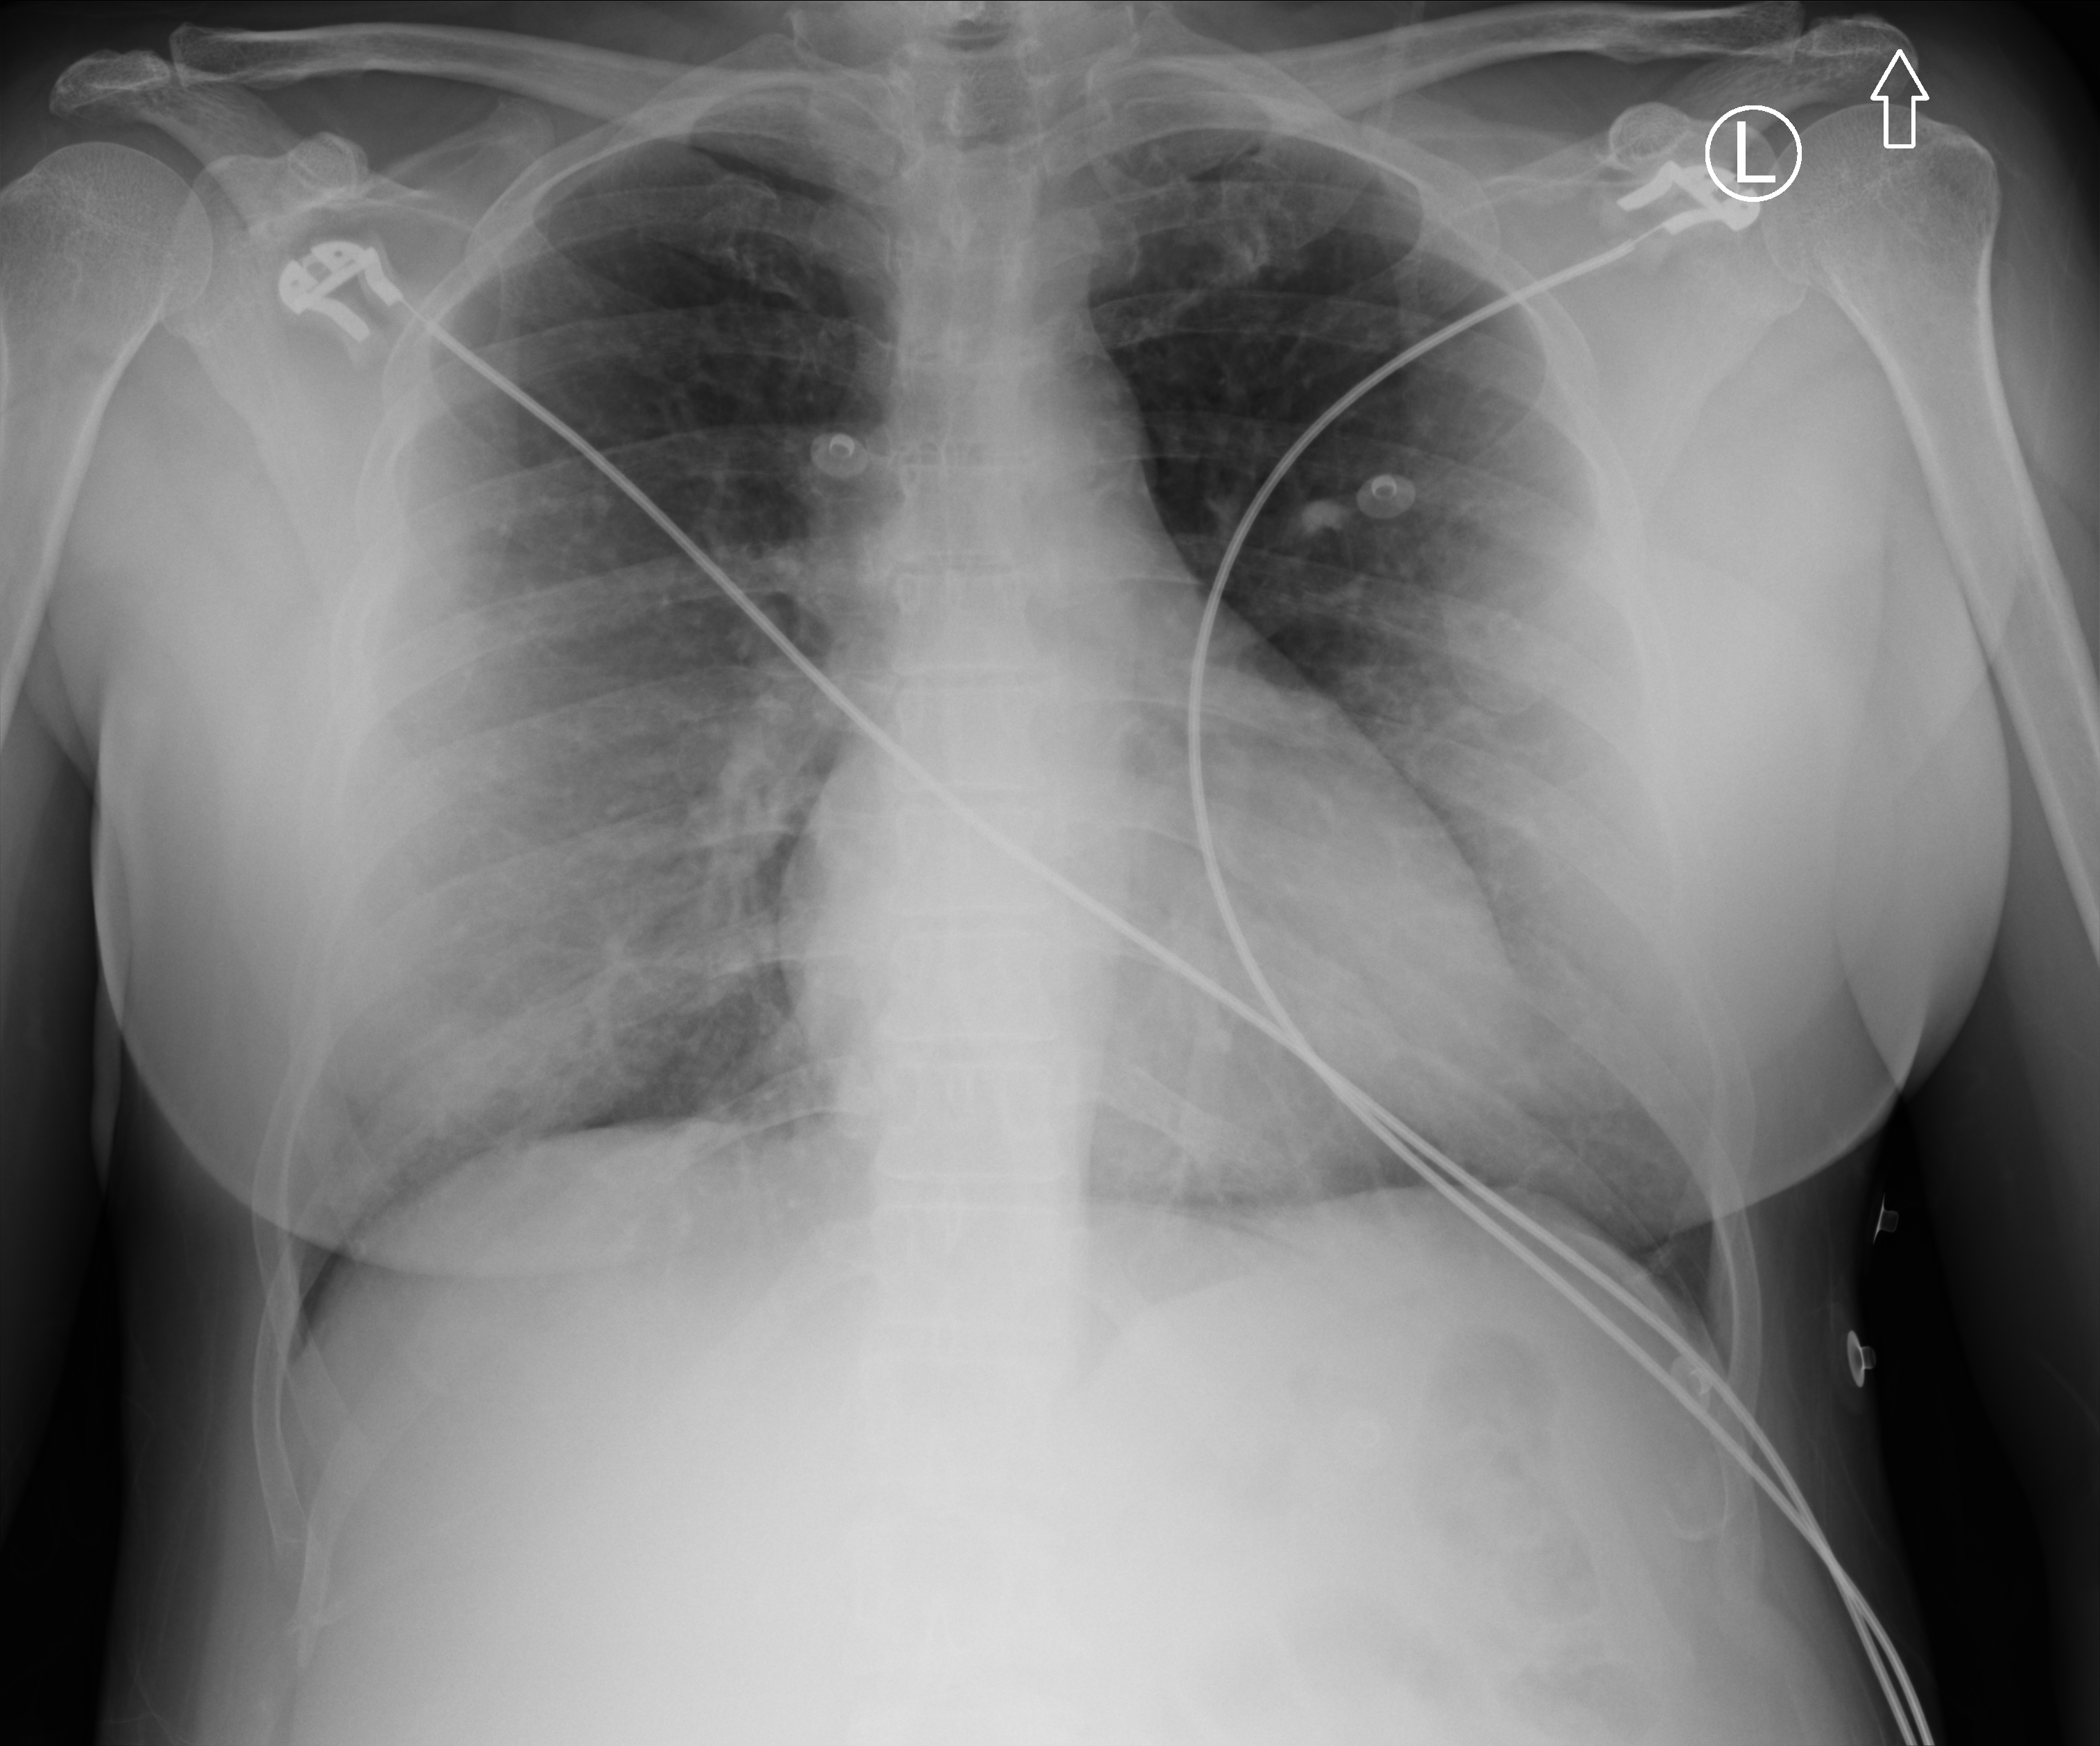
Chest X-ray (portable). Patient hospitalised with COVID-19; female, aged 18–59 years.
From the hospital-stay record, not from the radiograph (when in the stay this image was taken is not recorded): mechanically ventilated during this hospital stay: no; smoking status (admission record): never.